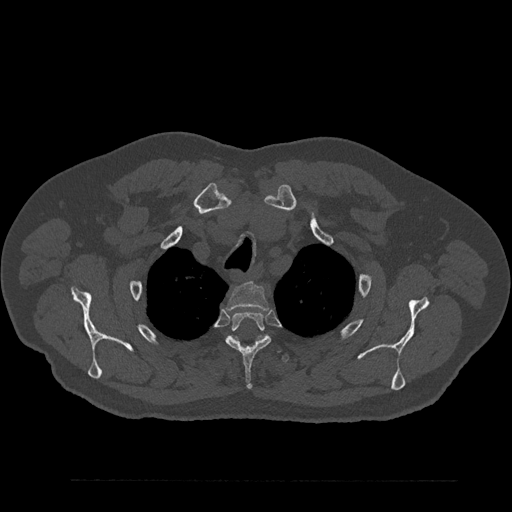
CT including the spine, one axial slice. Position 684 of 797 along the scan axis. 120 kVp. Bone window (W 1800 / L 400 HU). 0.5 mm slice thickness. 512 × 512 image matrix, field of view 430 × 430 mm. Male patient, age 61 years. From the clinical record (not read from this slice): primary cancer: prostate.
Outlined on this slice (semi-automatic segmentation, software-assisted and operator-edited):
- T2 vertebra: bounding box (x1, y1, x2, y2) in pixels: (227, 282, 268, 310)
- T3 vertebra: (225, 312, 271, 390)
- T4 vertebra: (232, 336, 290, 362)